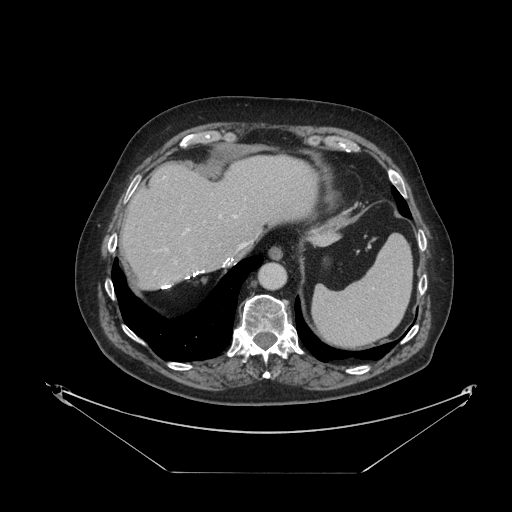
Contrast-enhanced abdominal CT, one axial slice; slice 94 of 121 in the series (ordered by position); reconstruction kernel STANDARD; 120 kVp; intravenous contrast given; soft-tissue window (W 400 / L 40 HU); 512 × 512 image matrix, field of view 500 × 500 mm. Male patient, age 68 years. From the clinical record (not read from this slice): diagnosis: colorectal cancer liver metastases, imaged before liver resection; multiple liver metastases: no; largest metastasis: 4 cm; disease in both lobes: no.
Structures marked on this image (outlined manually by an expert reader):
- hepatic veins: bounding box [x1, y1, x2, y2] px = [185, 215, 246, 247]
- liver: [122, 155, 330, 289]
- planned liver remnant (the part of the liver to remain after resection): [122, 155, 318, 288]
- portal vein (with intrahepatic branches): [165, 215, 222, 264]